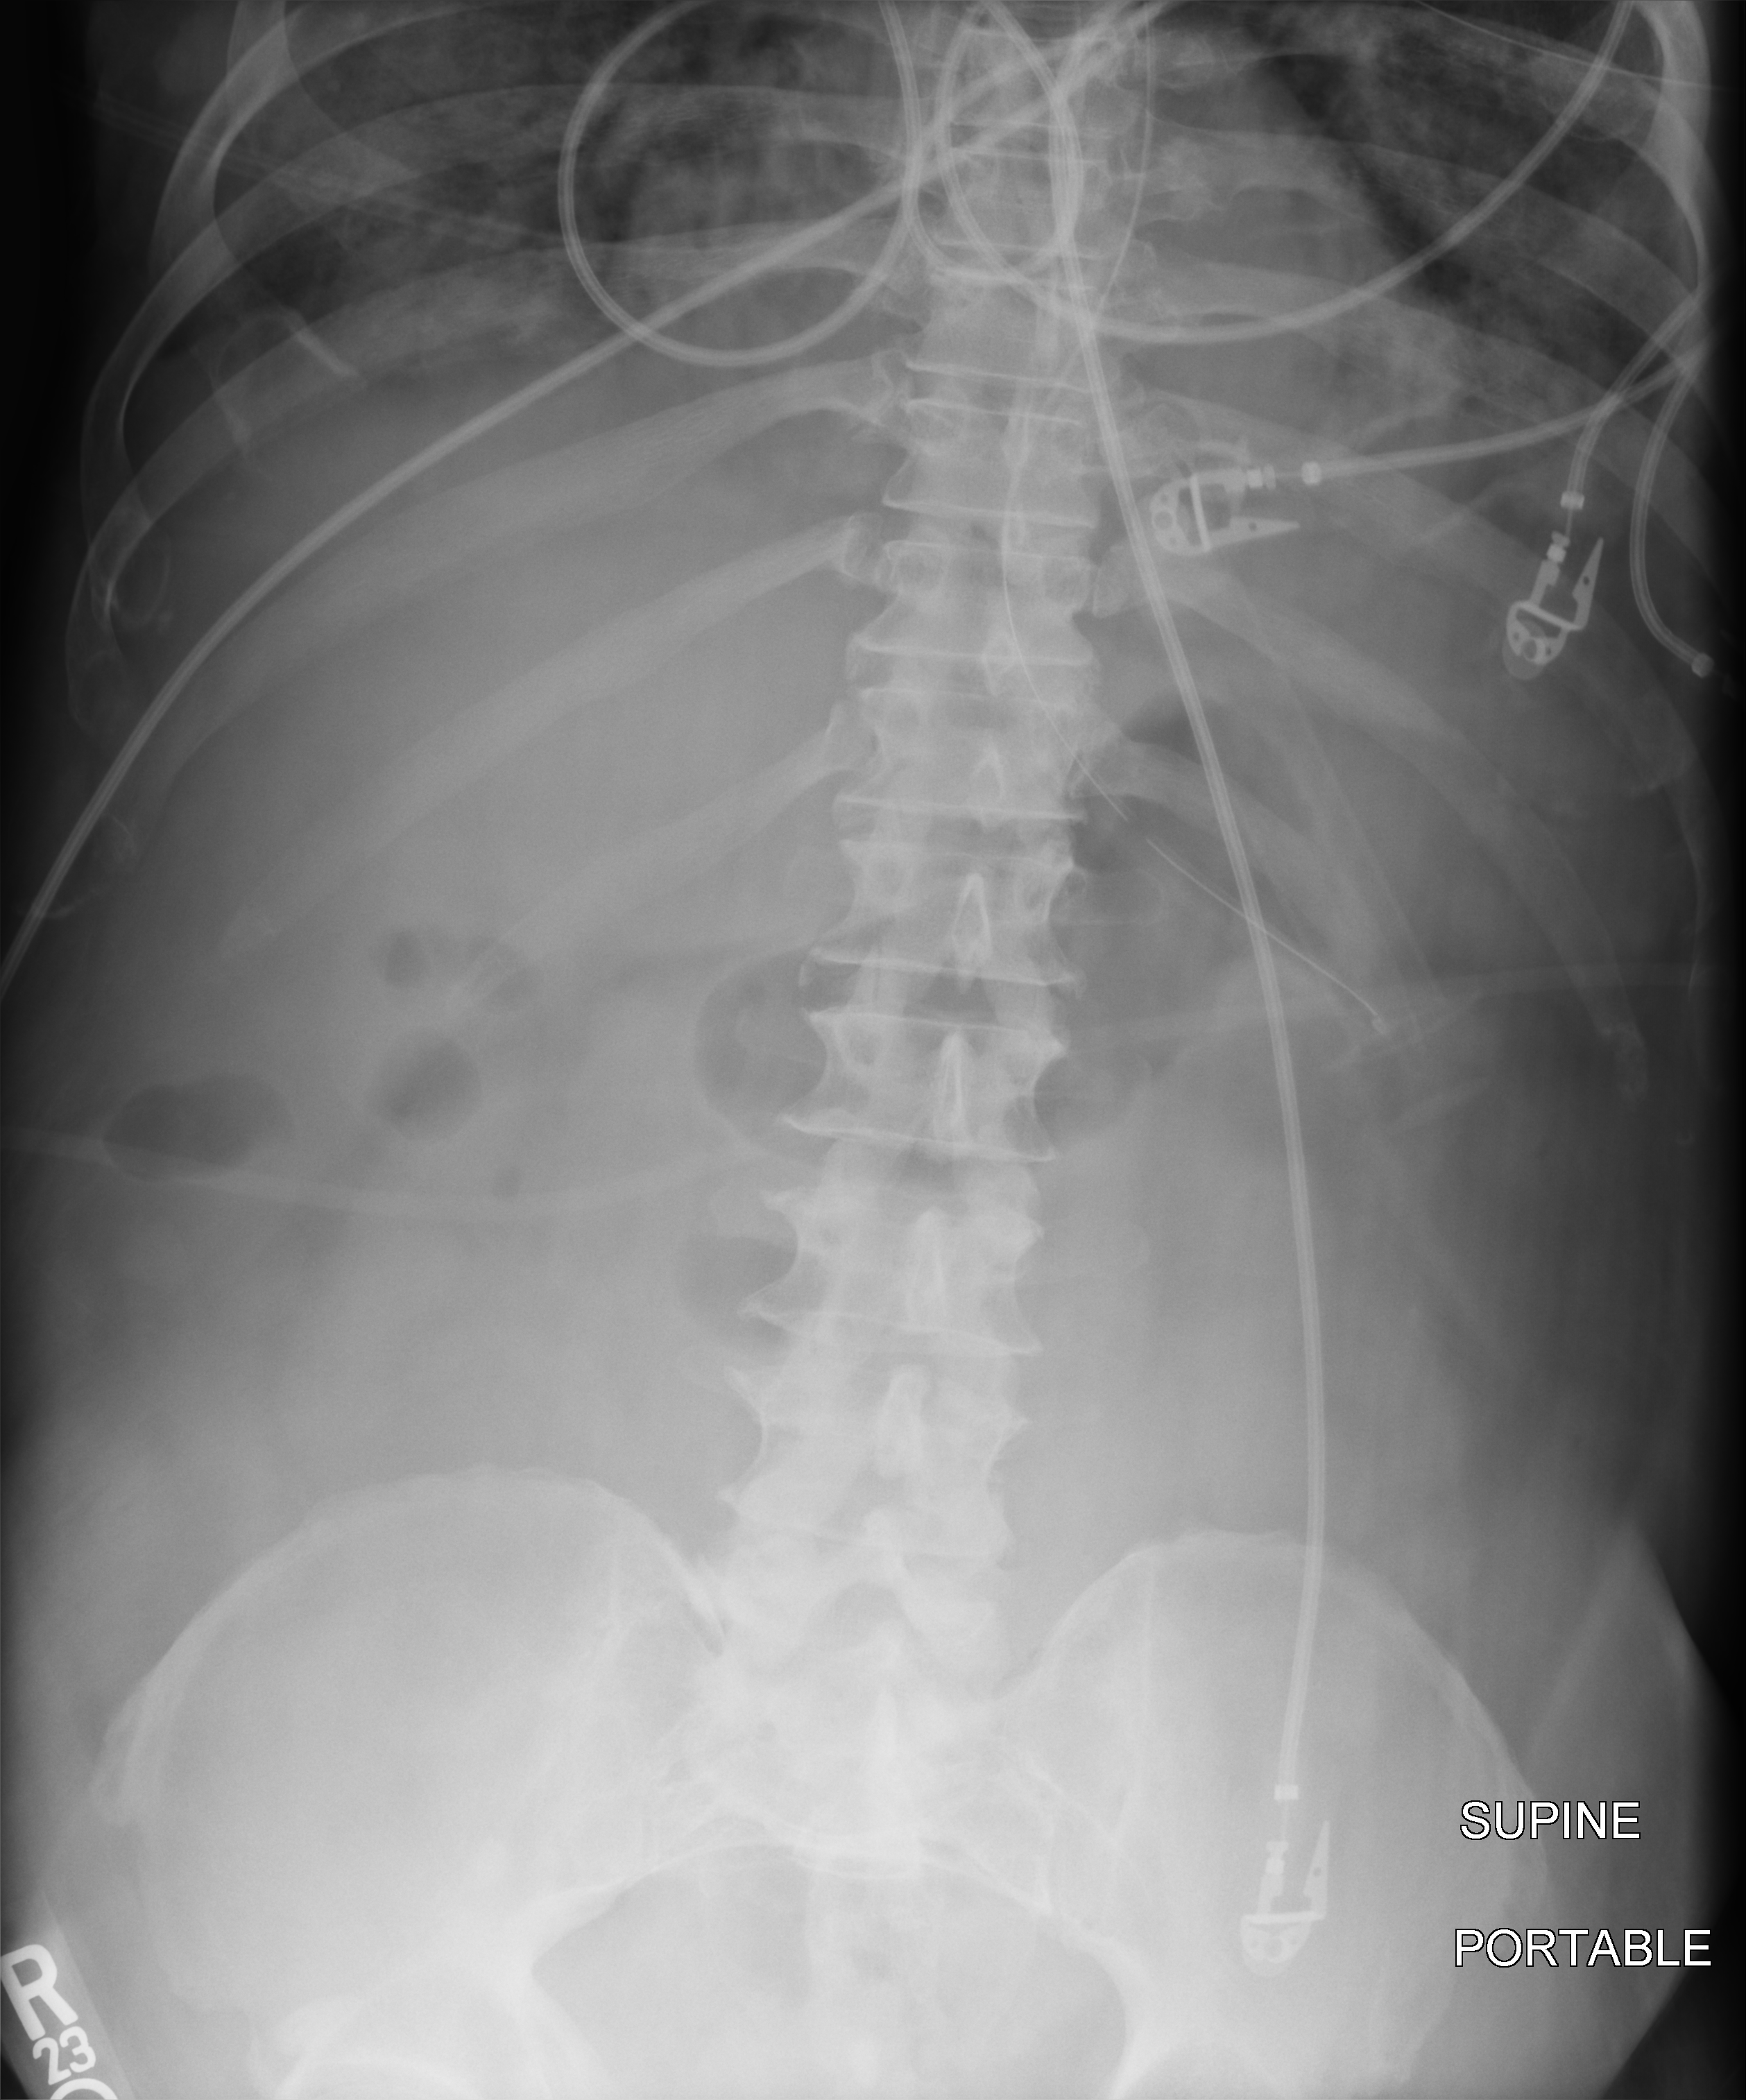
Abdomen X-ray (portable); anteroposterior (AP) projection. Male patient hospitalised with COVID-19, age 60–74 years.
From the hospital-stay record, not from the radiograph (when in the stay this image was taken is not recorded): admitted to intensive care during this hospital stay: yes.